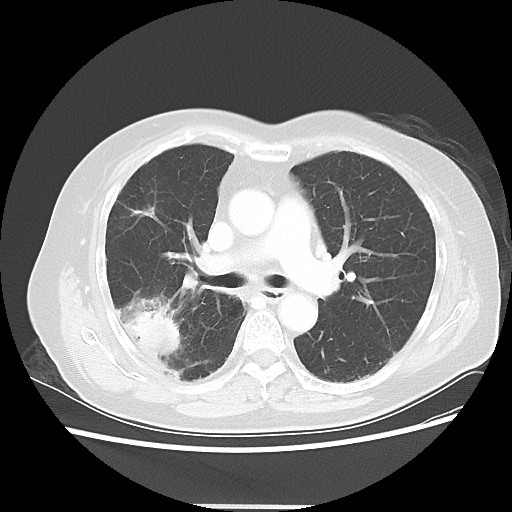
Chest CT, one axial slice. Slice 29 of 50 in the series (ordered by position). Reconstruction kernel LUNG. 120 kVp. Lung window (W 1500 / L -600 HU). 5 mm slice thickness. 512 × 512 image matrix. Patient: female, 72 years. Case-level facts recorded for this patient, not image findings: clinical TNM (as recorded): T2 N1 M0.
Annotated regions visible in this slice (bounding box drawn by a radiologist):
- lung tumour (recorded histology: adenocarcinoma): bounding box <123,311,181,358> (left, top, right, bottom; pixels)